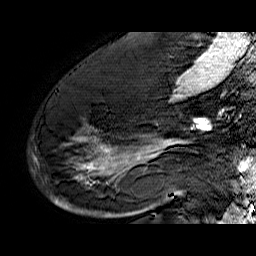
Breast MRI (dynamic contrast-enhanced), one sagittal slice; slice 36 of 60 in the series (ordered by position); dynamic contrast-enhanced series, time point 2 of 6 at this slice position (early post-contrast); 1.5 T; TE 6.4 ms, TR 32.9 ms; 4 mm slice thickness; 256 × 256 image matrix, field of view 200 × 200 mm. Female patient. Case-level facts recorded for this patient, not image findings: setting: breast cancer imaged before/during neoadjuvant chemotherapy; receptor status: HR-positive, HER2-negative.
Annotated regions visible in this slice (semi-automatic segmentation, software-assisted and operator-edited):
- analysis volume of interest (the breast-tissue region the enhancement analysis was run in; not a lesion): bounding box [x1, y1, x2, y2] px = [49, 74, 176, 210]
- tumour enhancement mask (voxels above the 100 % enhancement threshold inside the analysis volume of interest): [55, 92, 176, 203]